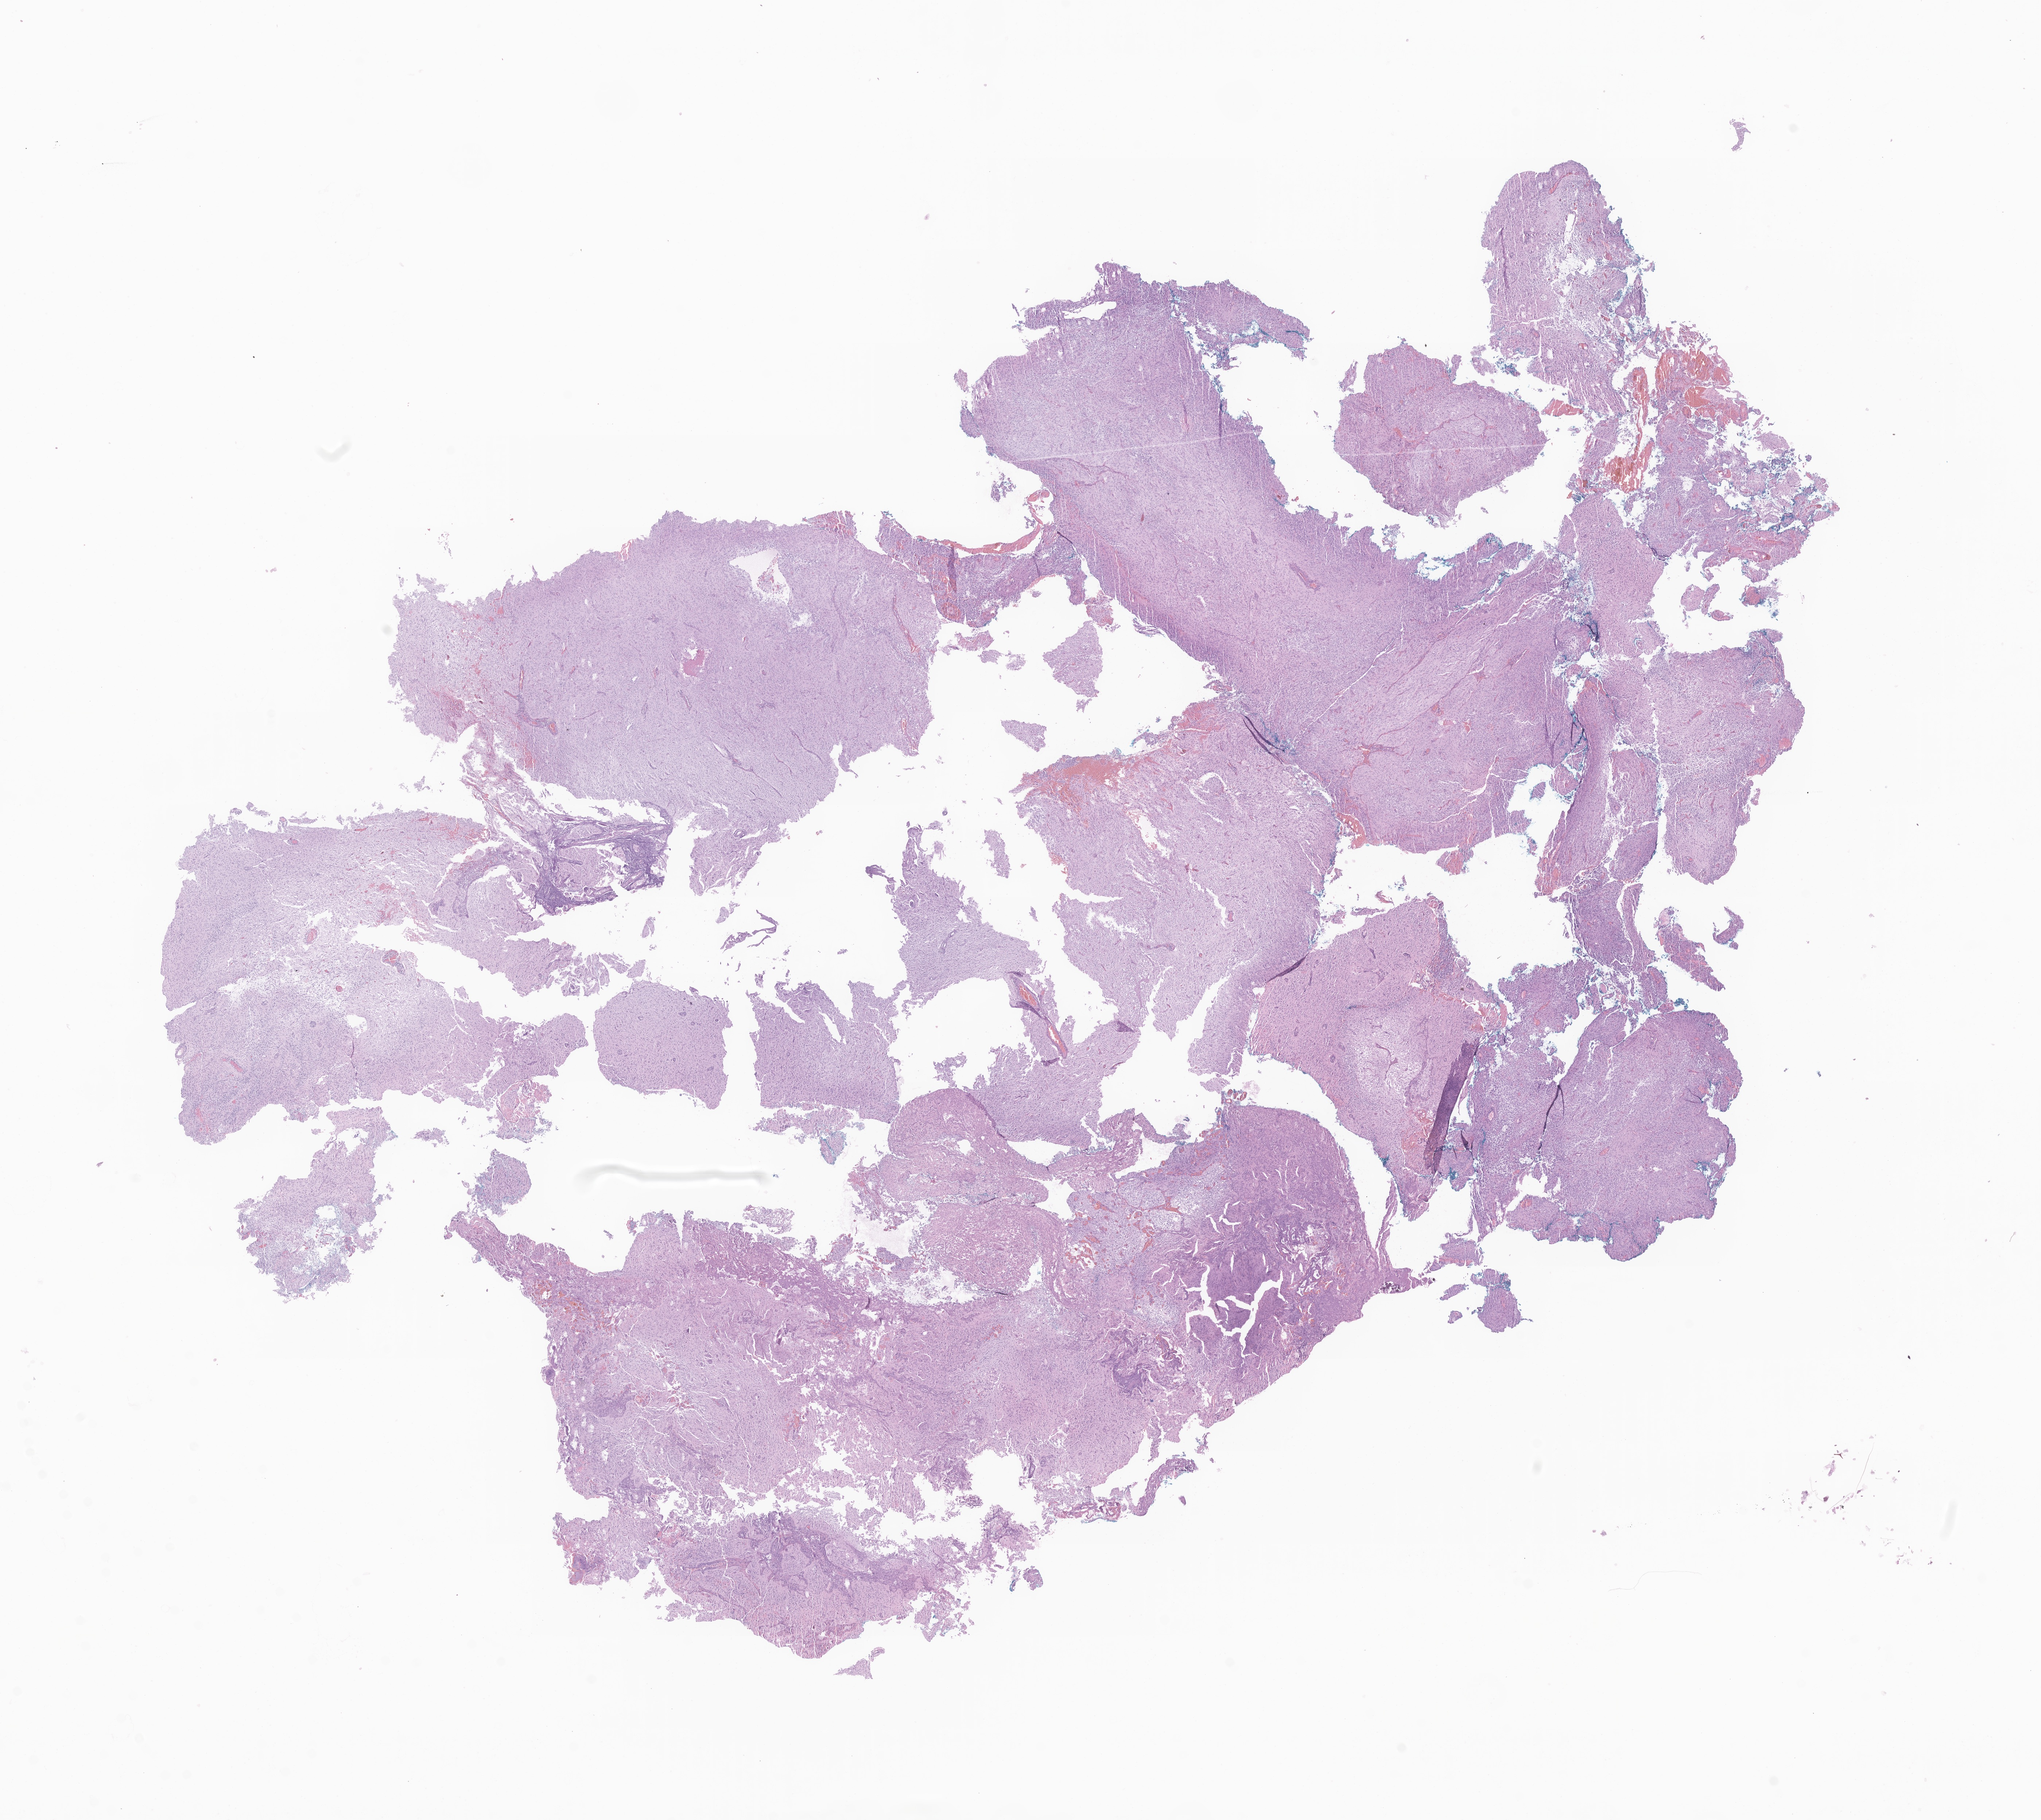
Hematoxylin and eosin (H&E) whole-slide image of tumor tissue from the frontal lobe — whole scanned area (about 23.6 x 21.0 mm) shown as a low-resolution overview; FFPE section. Male patient, age 164 months (13 years 8 months).
• recorded diagnosis: Glioma, malignant